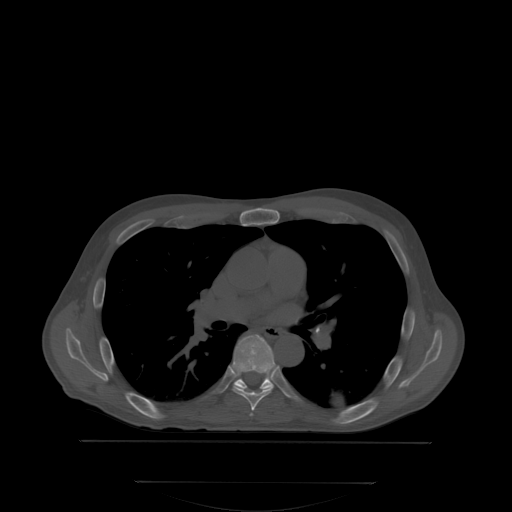
CT including the spine, one axial slice. Position 233 of 350 along the scan axis. Bone window (W 1800 / L 400 HU). 512 × 512 image matrix, field of view 500 × 500 mm. Male patient, age 58 years. Case-level facts recorded for this patient, not image findings: primary cancer: prostate.
Annotated regions visible in this slice (semi-automatic segmentation, software-assisted and operator-edited):
- T6 vertebra: bounding box (x1, y1, x2, y2) in pixels: (229, 335, 274, 411)
- T7 vertebra: (233, 335, 274, 391)